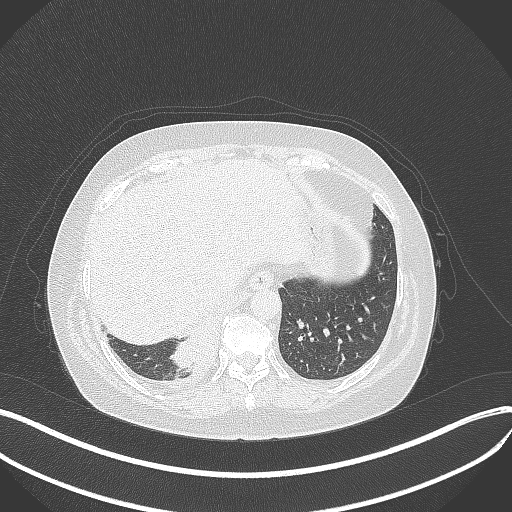
Chest CT, one axial slice; position 83 of 381 along the scan axis; reconstruction kernel B70f; 120 kVp; lung window (W 1500 / L -600 HU); 512 × 512 image matrix, field of view 400 × 400 mm. Female patient, age 56 years. Case-level facts recorded for this patient, not image findings: clinical TNM (as recorded): T2b N1 M0; histopathological grade: G3.
Outlined on this slice (rectangle marked by the reading radiologist):
- lung tumour (recorded histology: small cell carcinoma): bounding box [x1, y1, x2, y2] px = [174, 325, 219, 370]